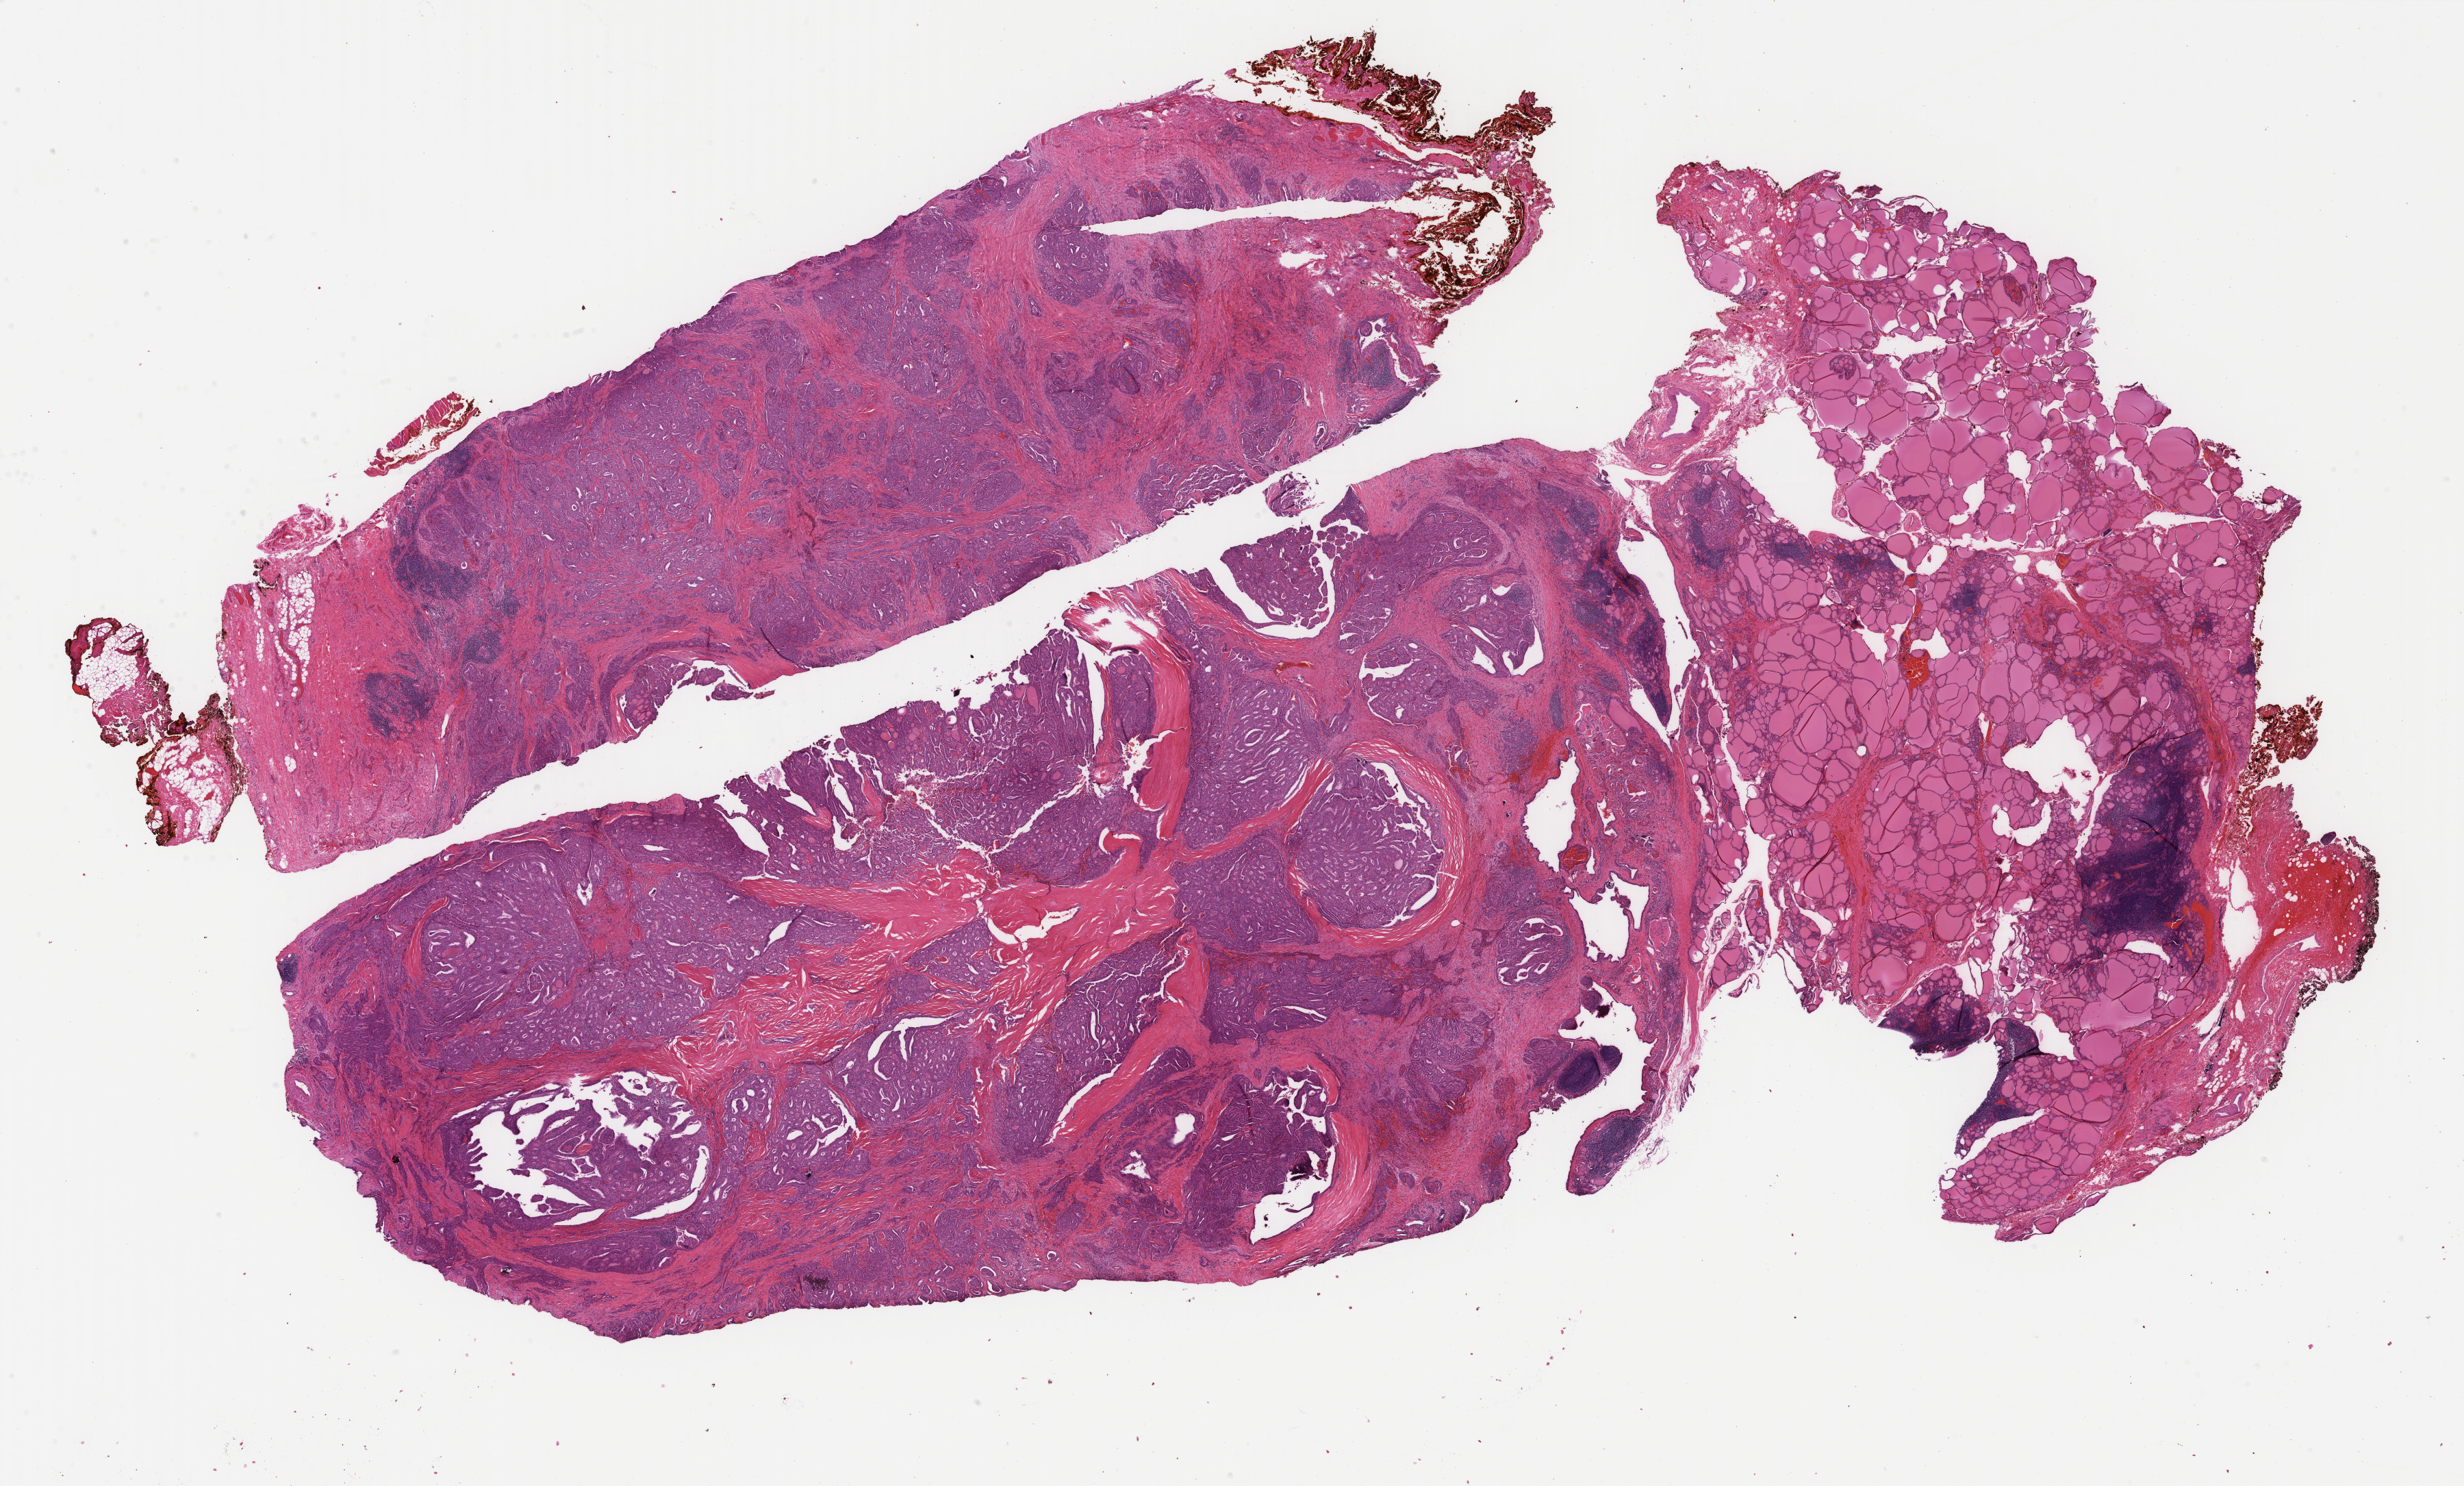
H&E-stained whole-slide image, a low-resolution overview of the entire scanned area, about 28.6 x 17.2 mm (slide scanned at 40x); formalin-fixed paraffin-embedded (FFPE) diagnostic section; thyroid, primary tumour sample. Male patient; age at initial diagnosis 38 years.
Histologic diagnosis: Papillary carcinoma, columnar cell (thyroid gland).